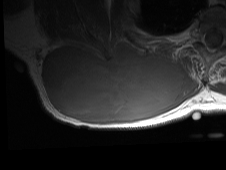
MRI of an extremity soft-tissue mass, one axial slice; position 38 of 81 along the scan axis; MR volume resampled by the dataset authors to the PET/CT grid (not the native acquisition matrix); 3.27 mm slice thickness; 226 × 170 image matrix, field of view 221 × 166 mm. Male patient. From the clinical record (not read from this slice): histological type: pleiomorphic spindle cell undifferentiated; grade: high; site of the primary tumour: right parascapusular.
Outlined on this slice (expert contour drawn on MRI and transferred to this co-registered scan by the dataset authors):
- gross tumour volume including surrounding oedema: bounding box [x1, y1, x2, y2] px = [39, 42, 198, 126]
- gross tumour volume (mass): [41, 43, 184, 123]